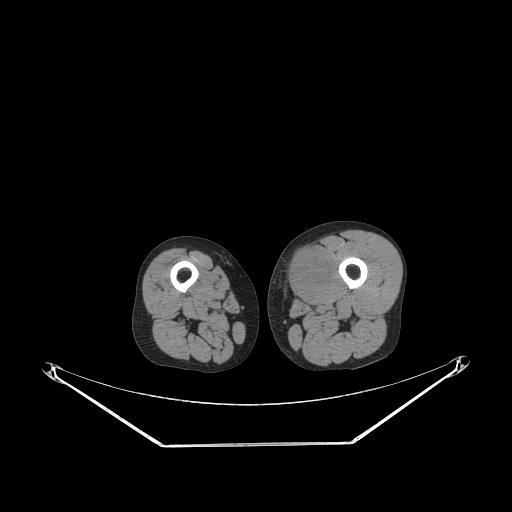
CT of an extremity soft-tissue mass (from a PET/CT study), one axial slice; slice 220 of 267 in the series (ordered by position); reconstruction kernel STANDARD; 140 kVp; soft-tissue window (W 400 / L 40 HU); 3.75 mm slice thickness; 512 × 512 image matrix, field of view 500 × 500 mm. Male patient. From the clinical record (not read from this slice): histological type: pleiomorphic leiomyosarcoma; grade: high; site of the primary tumour: left thigh.
Structures marked on this image (expert contour drawn on MRI and transferred to this co-registered scan by the dataset authors):
- gross tumour volume including surrounding oedema: bounding box <285,249,330,300> (left, top, right, bottom; pixels)
- gross tumour volume (mass): <285,249,325,298>